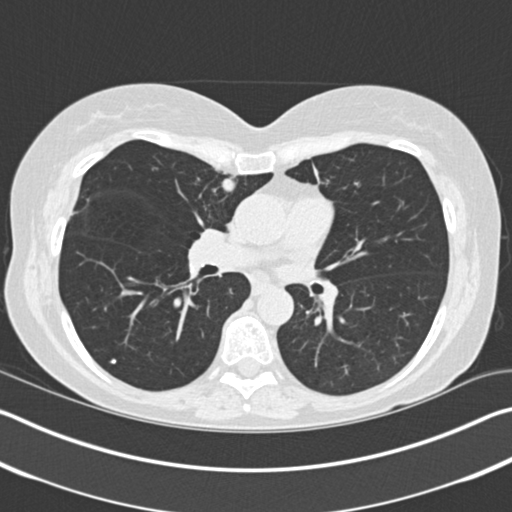
Low-dose screening chest CT, one axial slice. Position 99 of 183 along the scan axis. 120 kVp. Lung window (W 1500 / L -600 HU). 2 mm slice thickness. 512 × 512 image matrix, field of view 340 × 340 mm.
Outlined on this slice (outlined manually by an expert reader):
- lesion 1 (tumor, upper lobe of right lung): box from (x=222, y=177) to (x=235, y=192) px